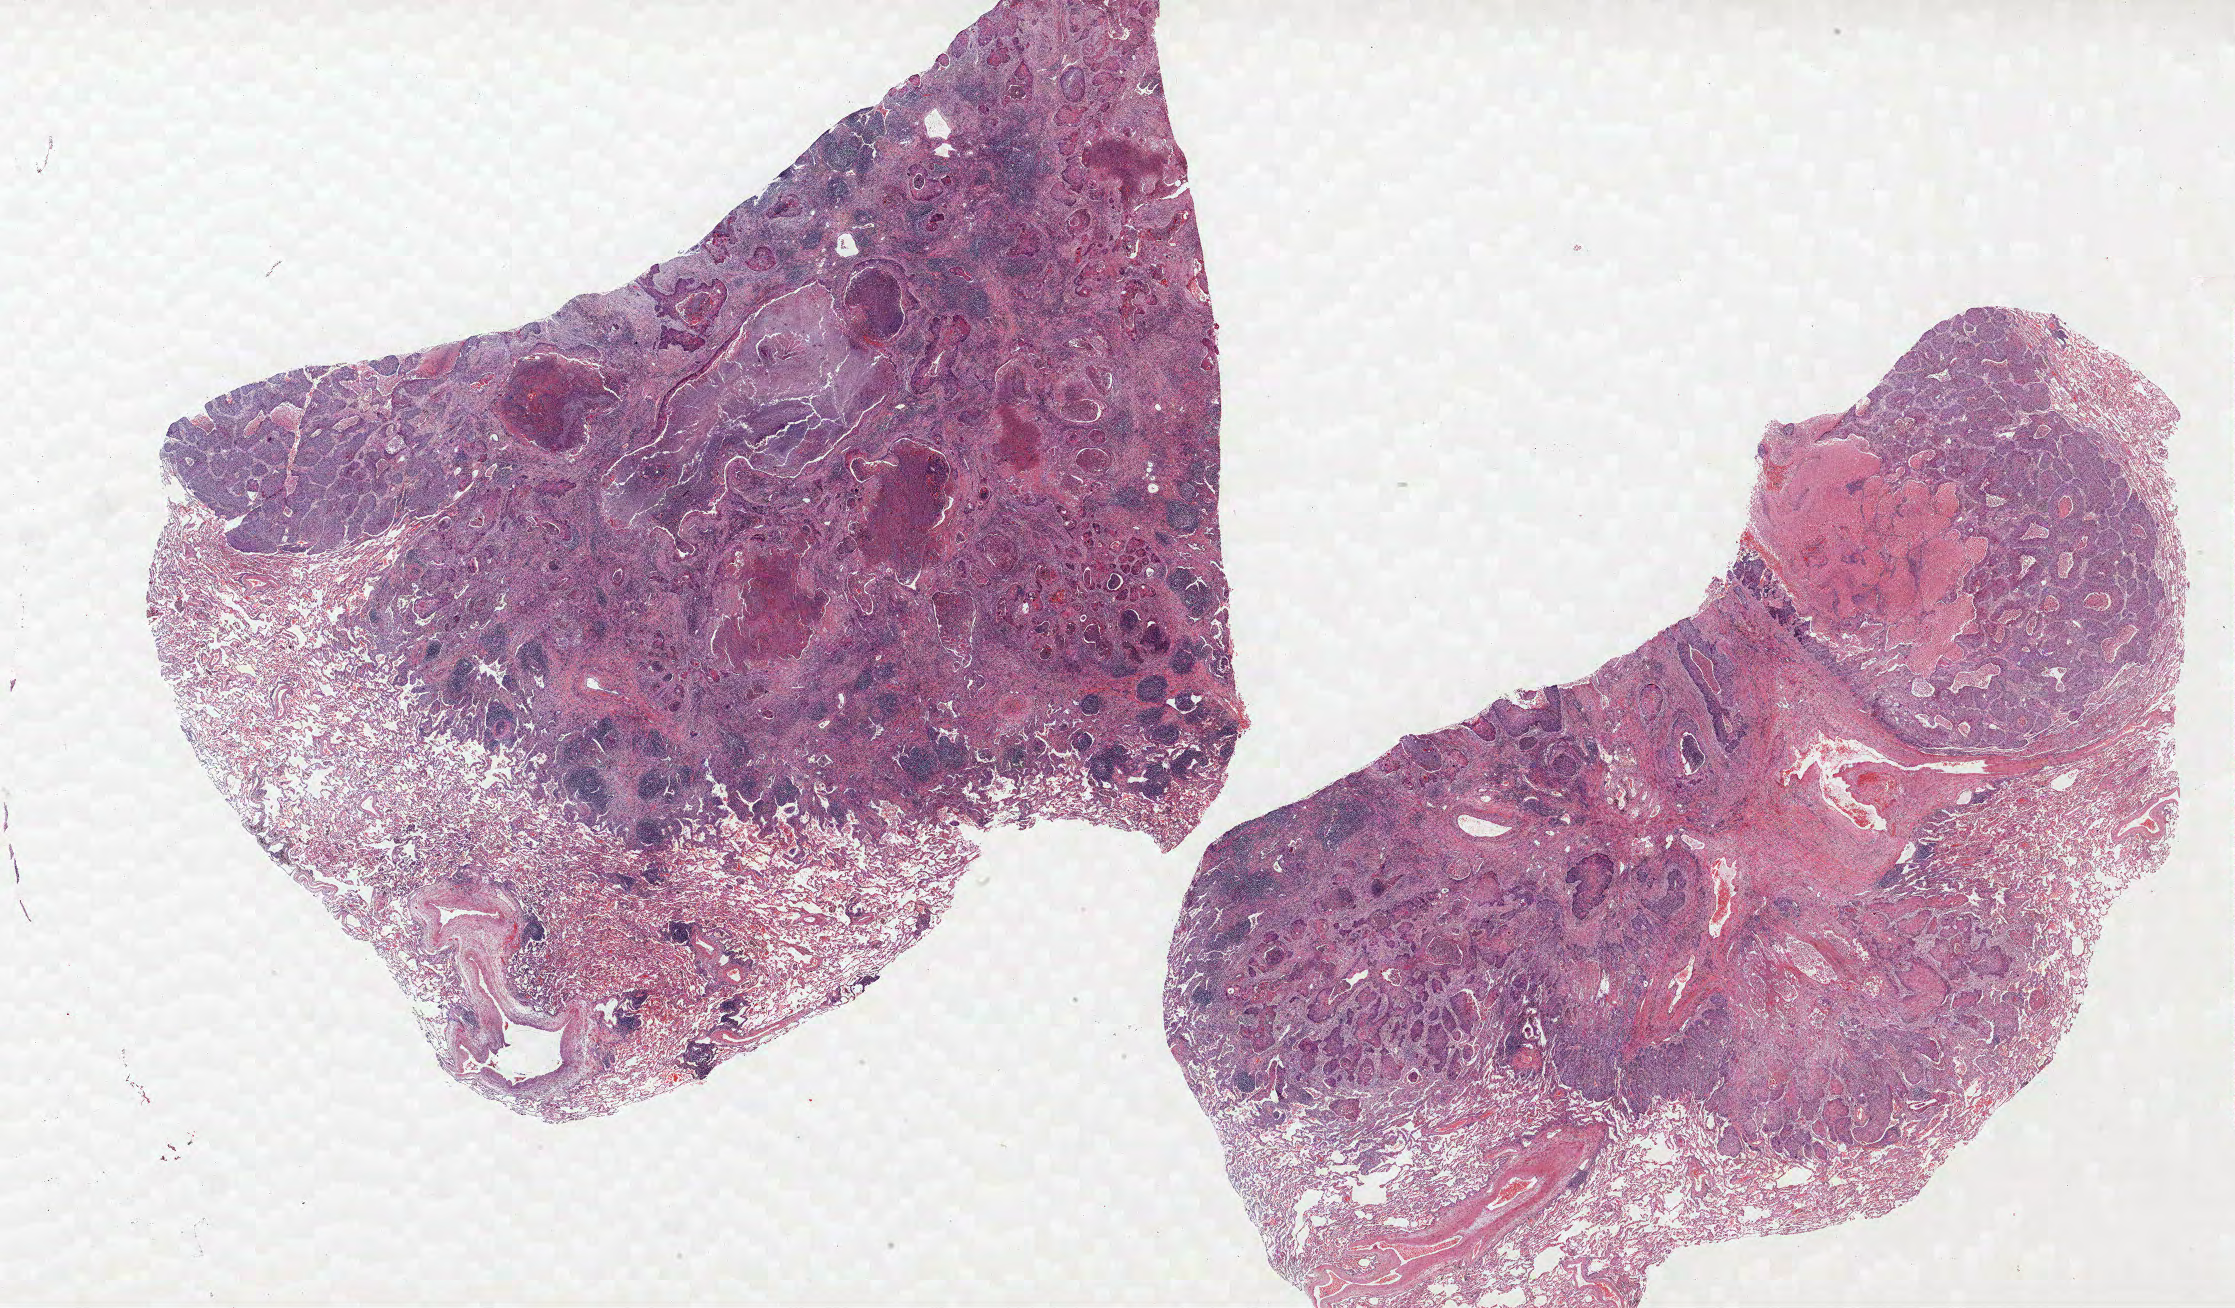
Whole-slide histology image, H&E, a low-resolution overview of the entire scanned area, about 35.8 x 20.9 mm. Formalin-fixed paraffin-embedded (FFPE) section. Lung tissue. Female, age 58 at enrolment. Former smoker at enrolment. Grade: moderately differentiated (G2).
Primary tumour location (clinical record): left upper lobe. Participant's lung-cancer diagnosis: Squamous cell carcinoma, NOS (ICD-O-3 8070/3). Tumour size (pathology): 22 mm. ICD-O-3 topography: upper lobe of lung (C34.1). Stage (AJCC 6th edition): IA.